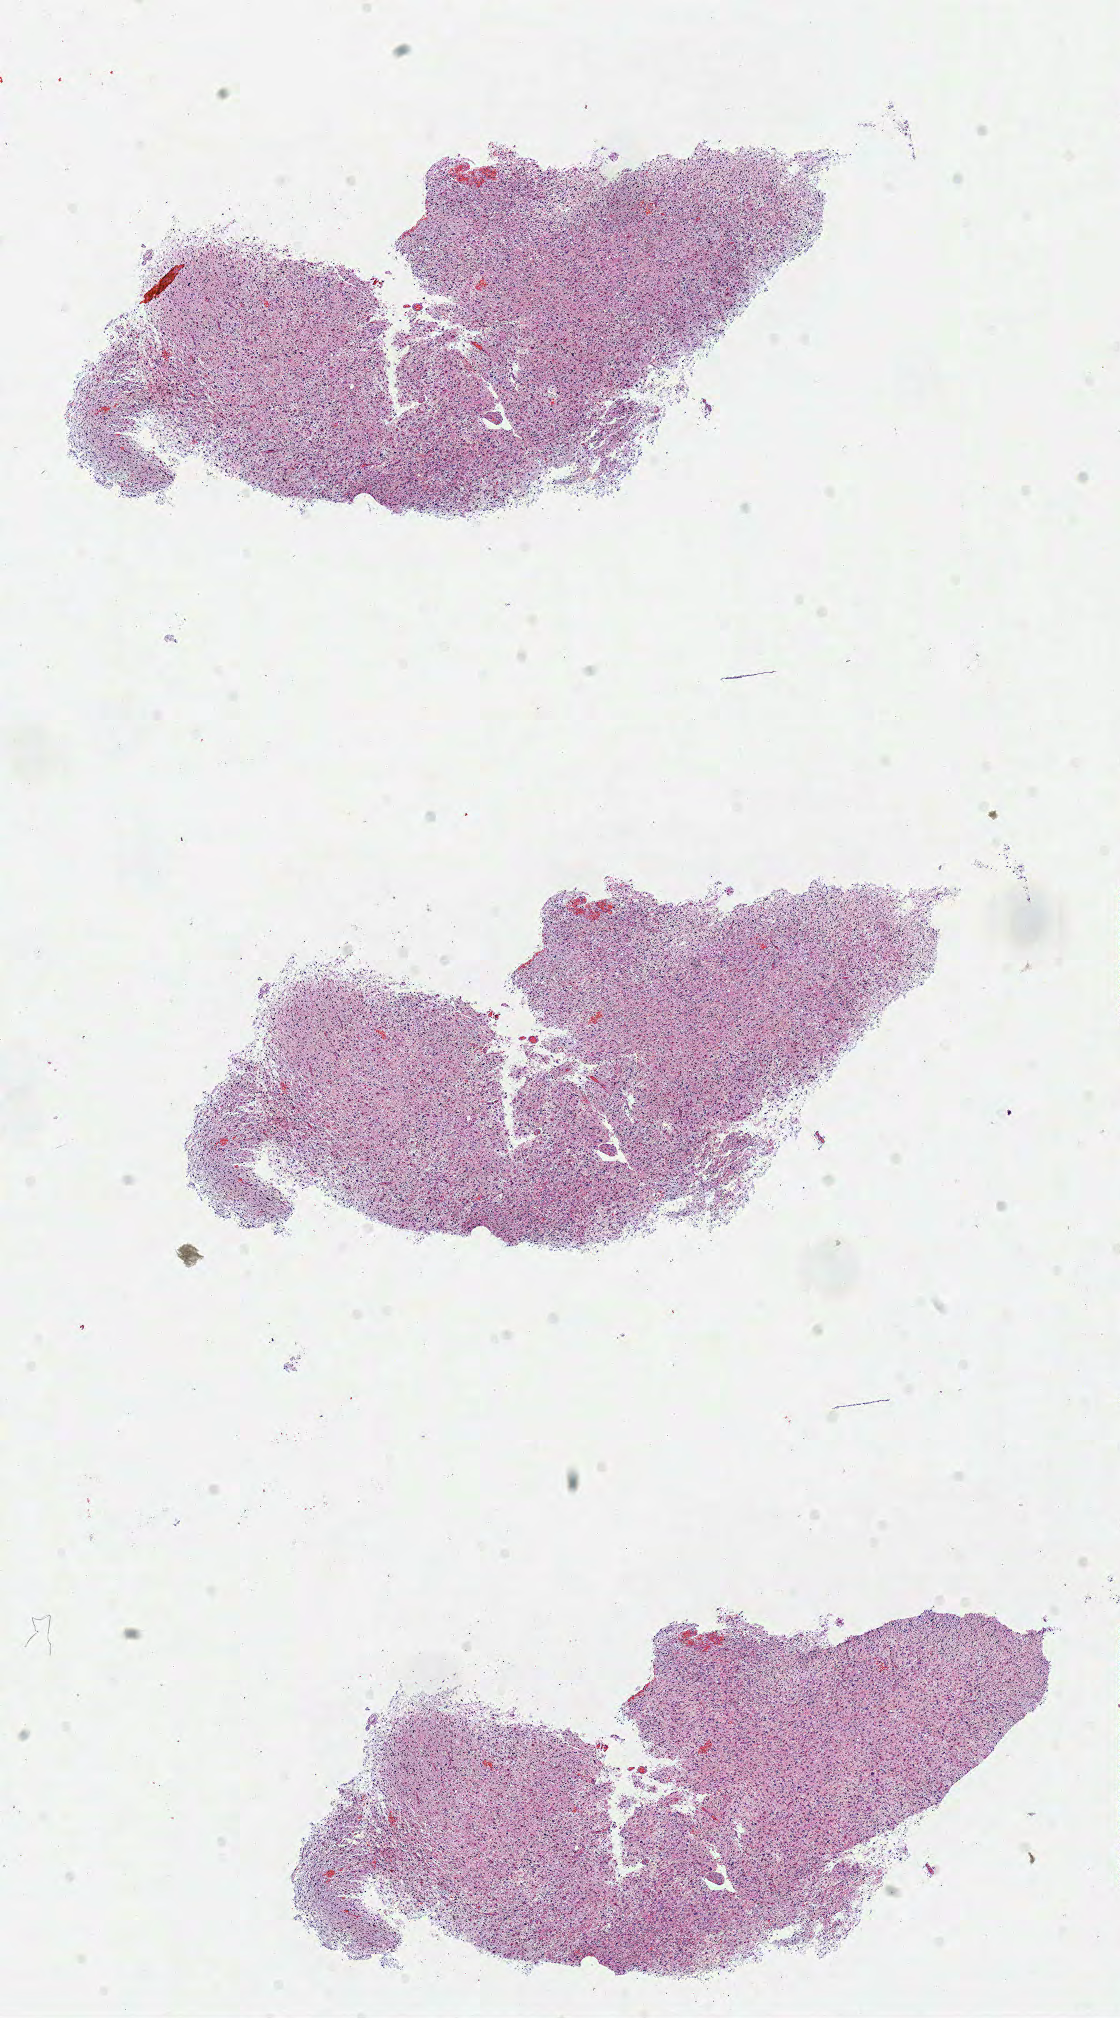
Hematoxylin and eosin (H&E) stained whole-slide image, low-resolution overview of the scanned area, about 8.8 x 15.9 mm (from a 40x scan); frozen section from the top of the tissue portion; primary tumour sample from the brain. Female patient; age at initial diagnosis 49 years. Composition of this section per pathologist review: tumour cells 100%, tumour nuclei 80%, normal cells 0%, stromal cells 0%, necrosis 0%.
Histologic diagnosis: Glioblastoma.